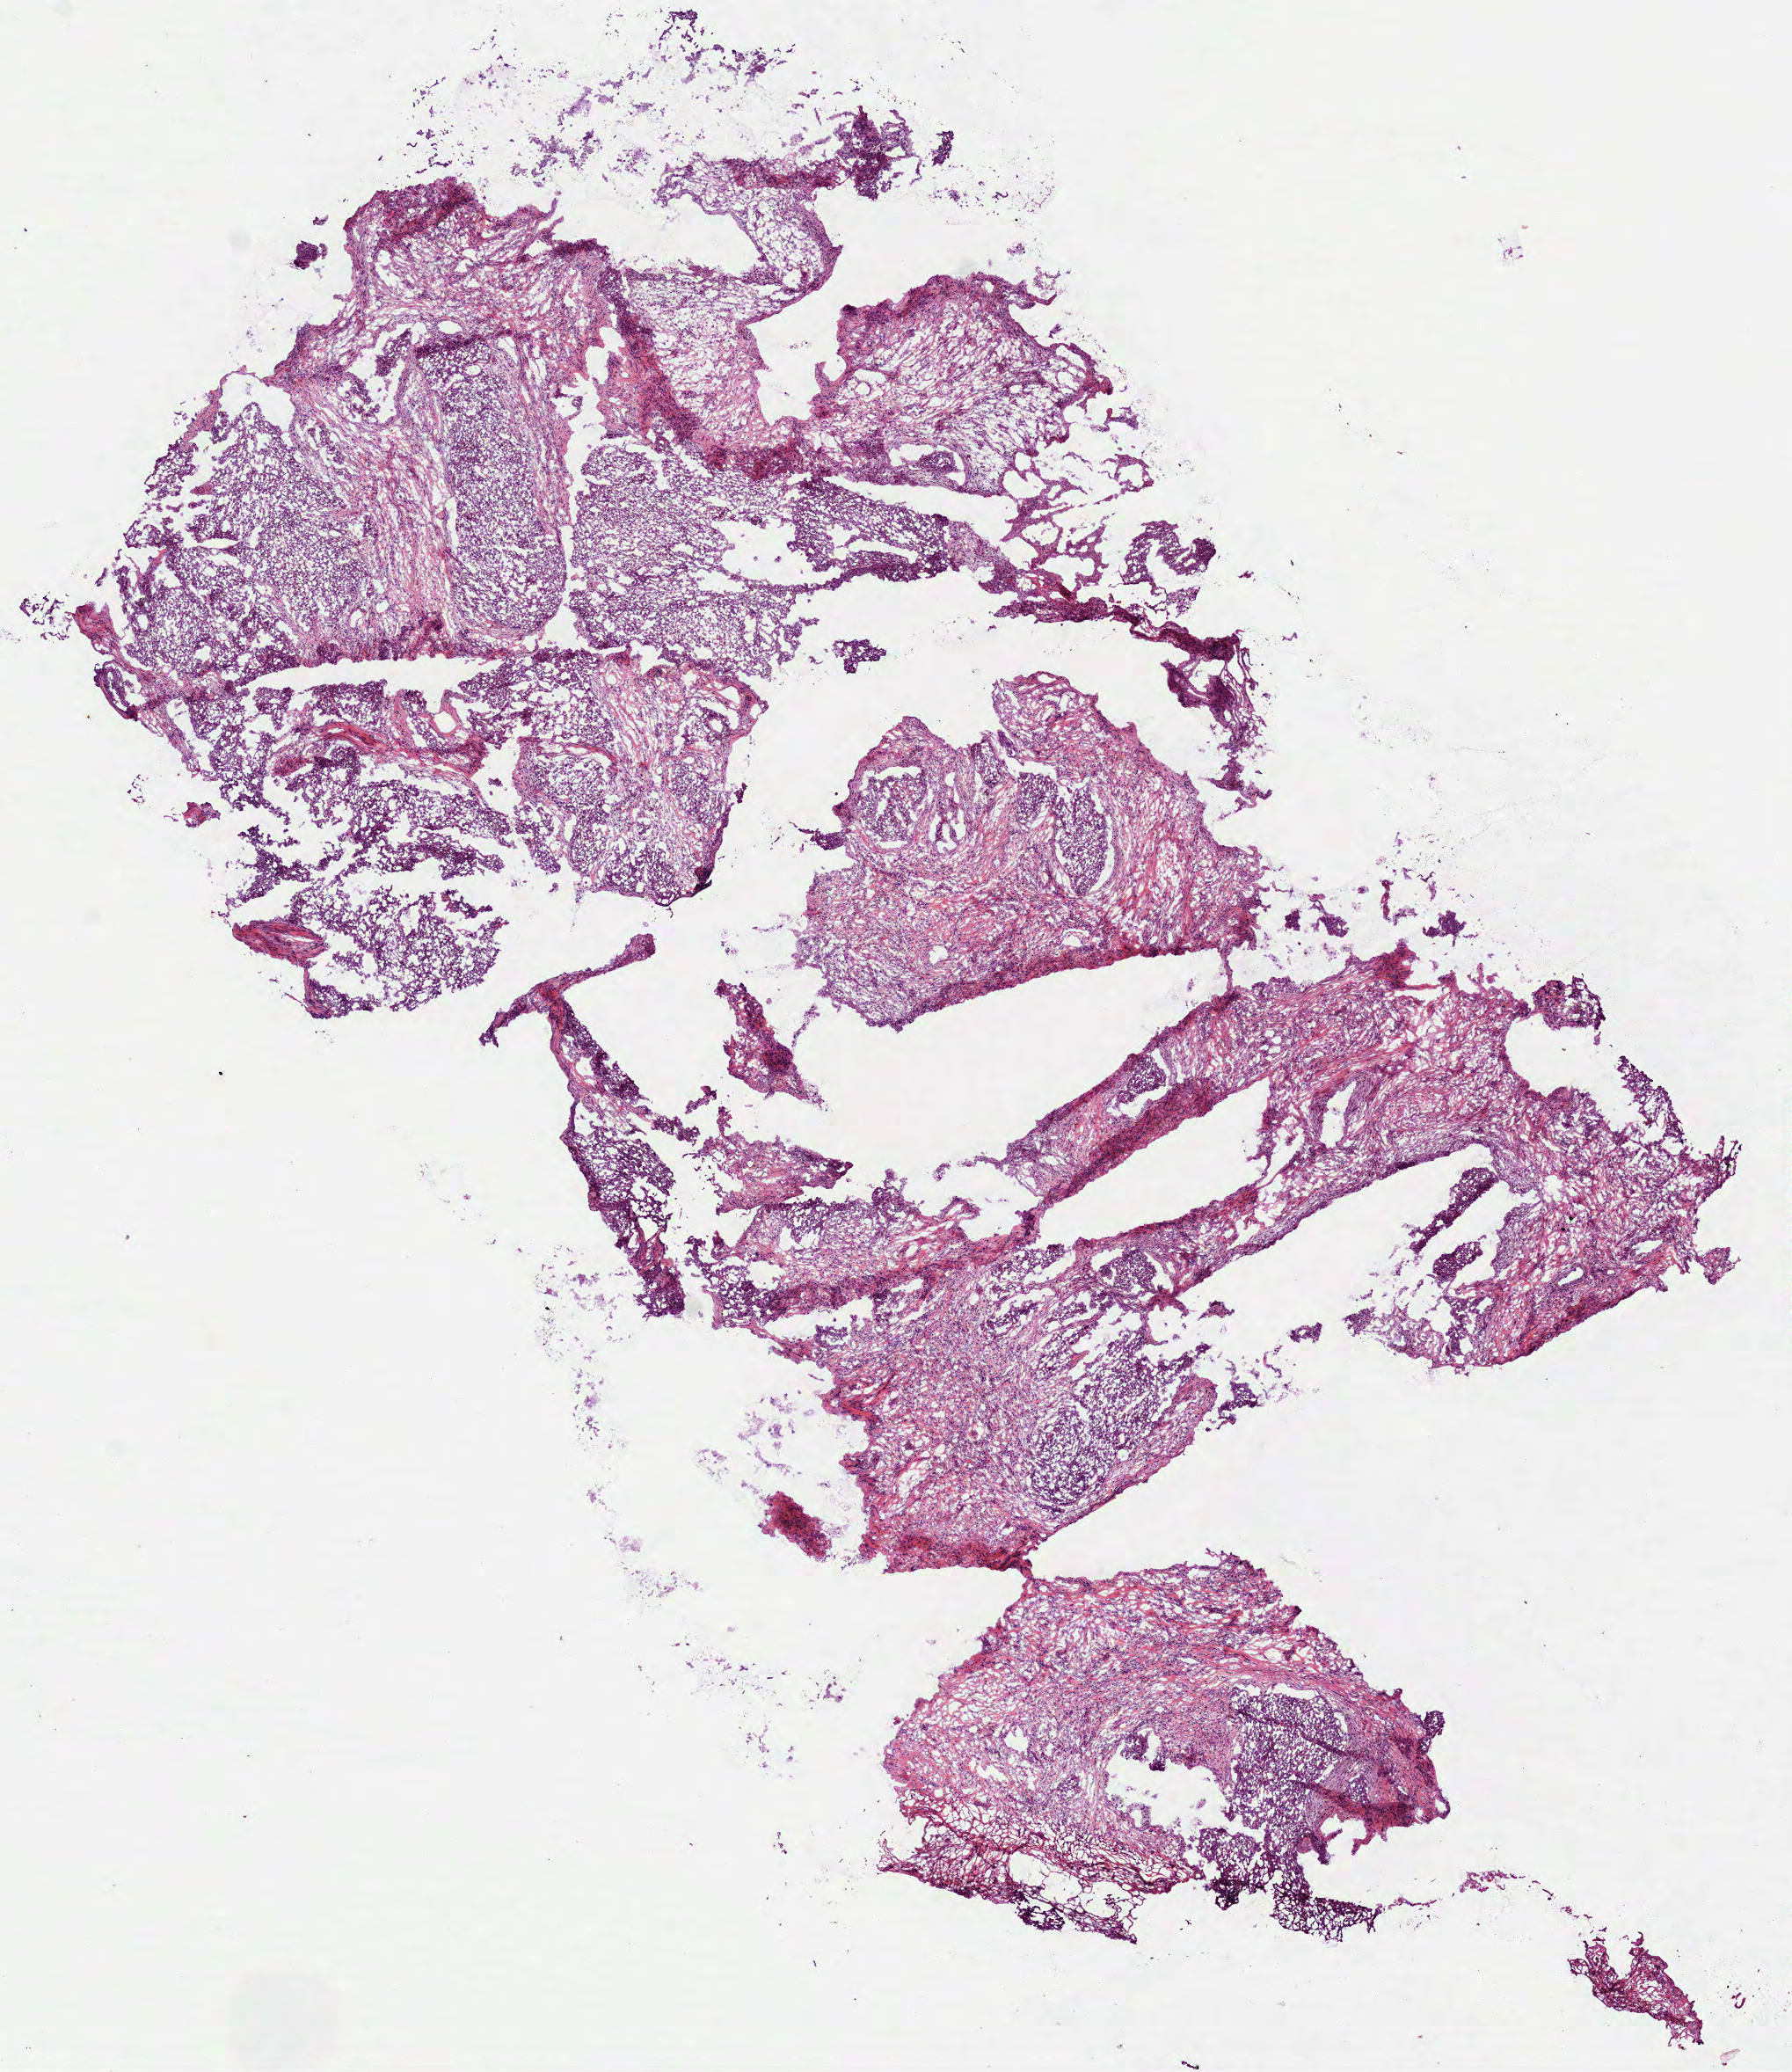
H&E-stained whole-slide image — low-resolution overview of the scanned area, about 8.2 x 9.5 mm, frozen section from the top of the tissue portion, sample: primary tumour, head and neck. Male, age 67 years at initial diagnosis. Histologic grade: G3 (poorly differentiated). Composition of this section per pathologist review: tumour cells 60%, tumour nuclei 60%, normal cells 0%, stromal cells 40%, necrosis 0%.
AJCC pathologic stage: II. Diagnosis: Squamous cell carcinoma, NOS (floor of mouth, NOS).